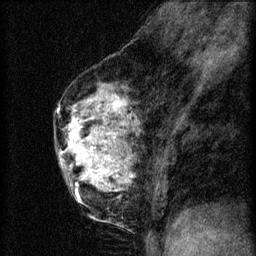
Breast MRI (dynamic contrast-enhanced), one sagittal slice; slice 37 of 60 in the series (ordered by position); 3 images stored at this slice position (order not interpretable as contrast timing); 1.5 T; TE 4.2 ms, TR 8.2 ms; 2 mm slice thickness; 256 × 256 image matrix. Female patient, age 56 years.
Structures marked on this image (semi-automatically segmented with operator editing):
- analysis volume of interest (the breast-tissue region the enhancement analysis was run in; not a lesion): bounding box (x1, y1, x2, y2) in pixels: (60, 124, 114, 179)
- tumour enhancement mask (voxels above the 70 % enhancement threshold inside the analysis volume of interest): (82, 150, 93, 179)